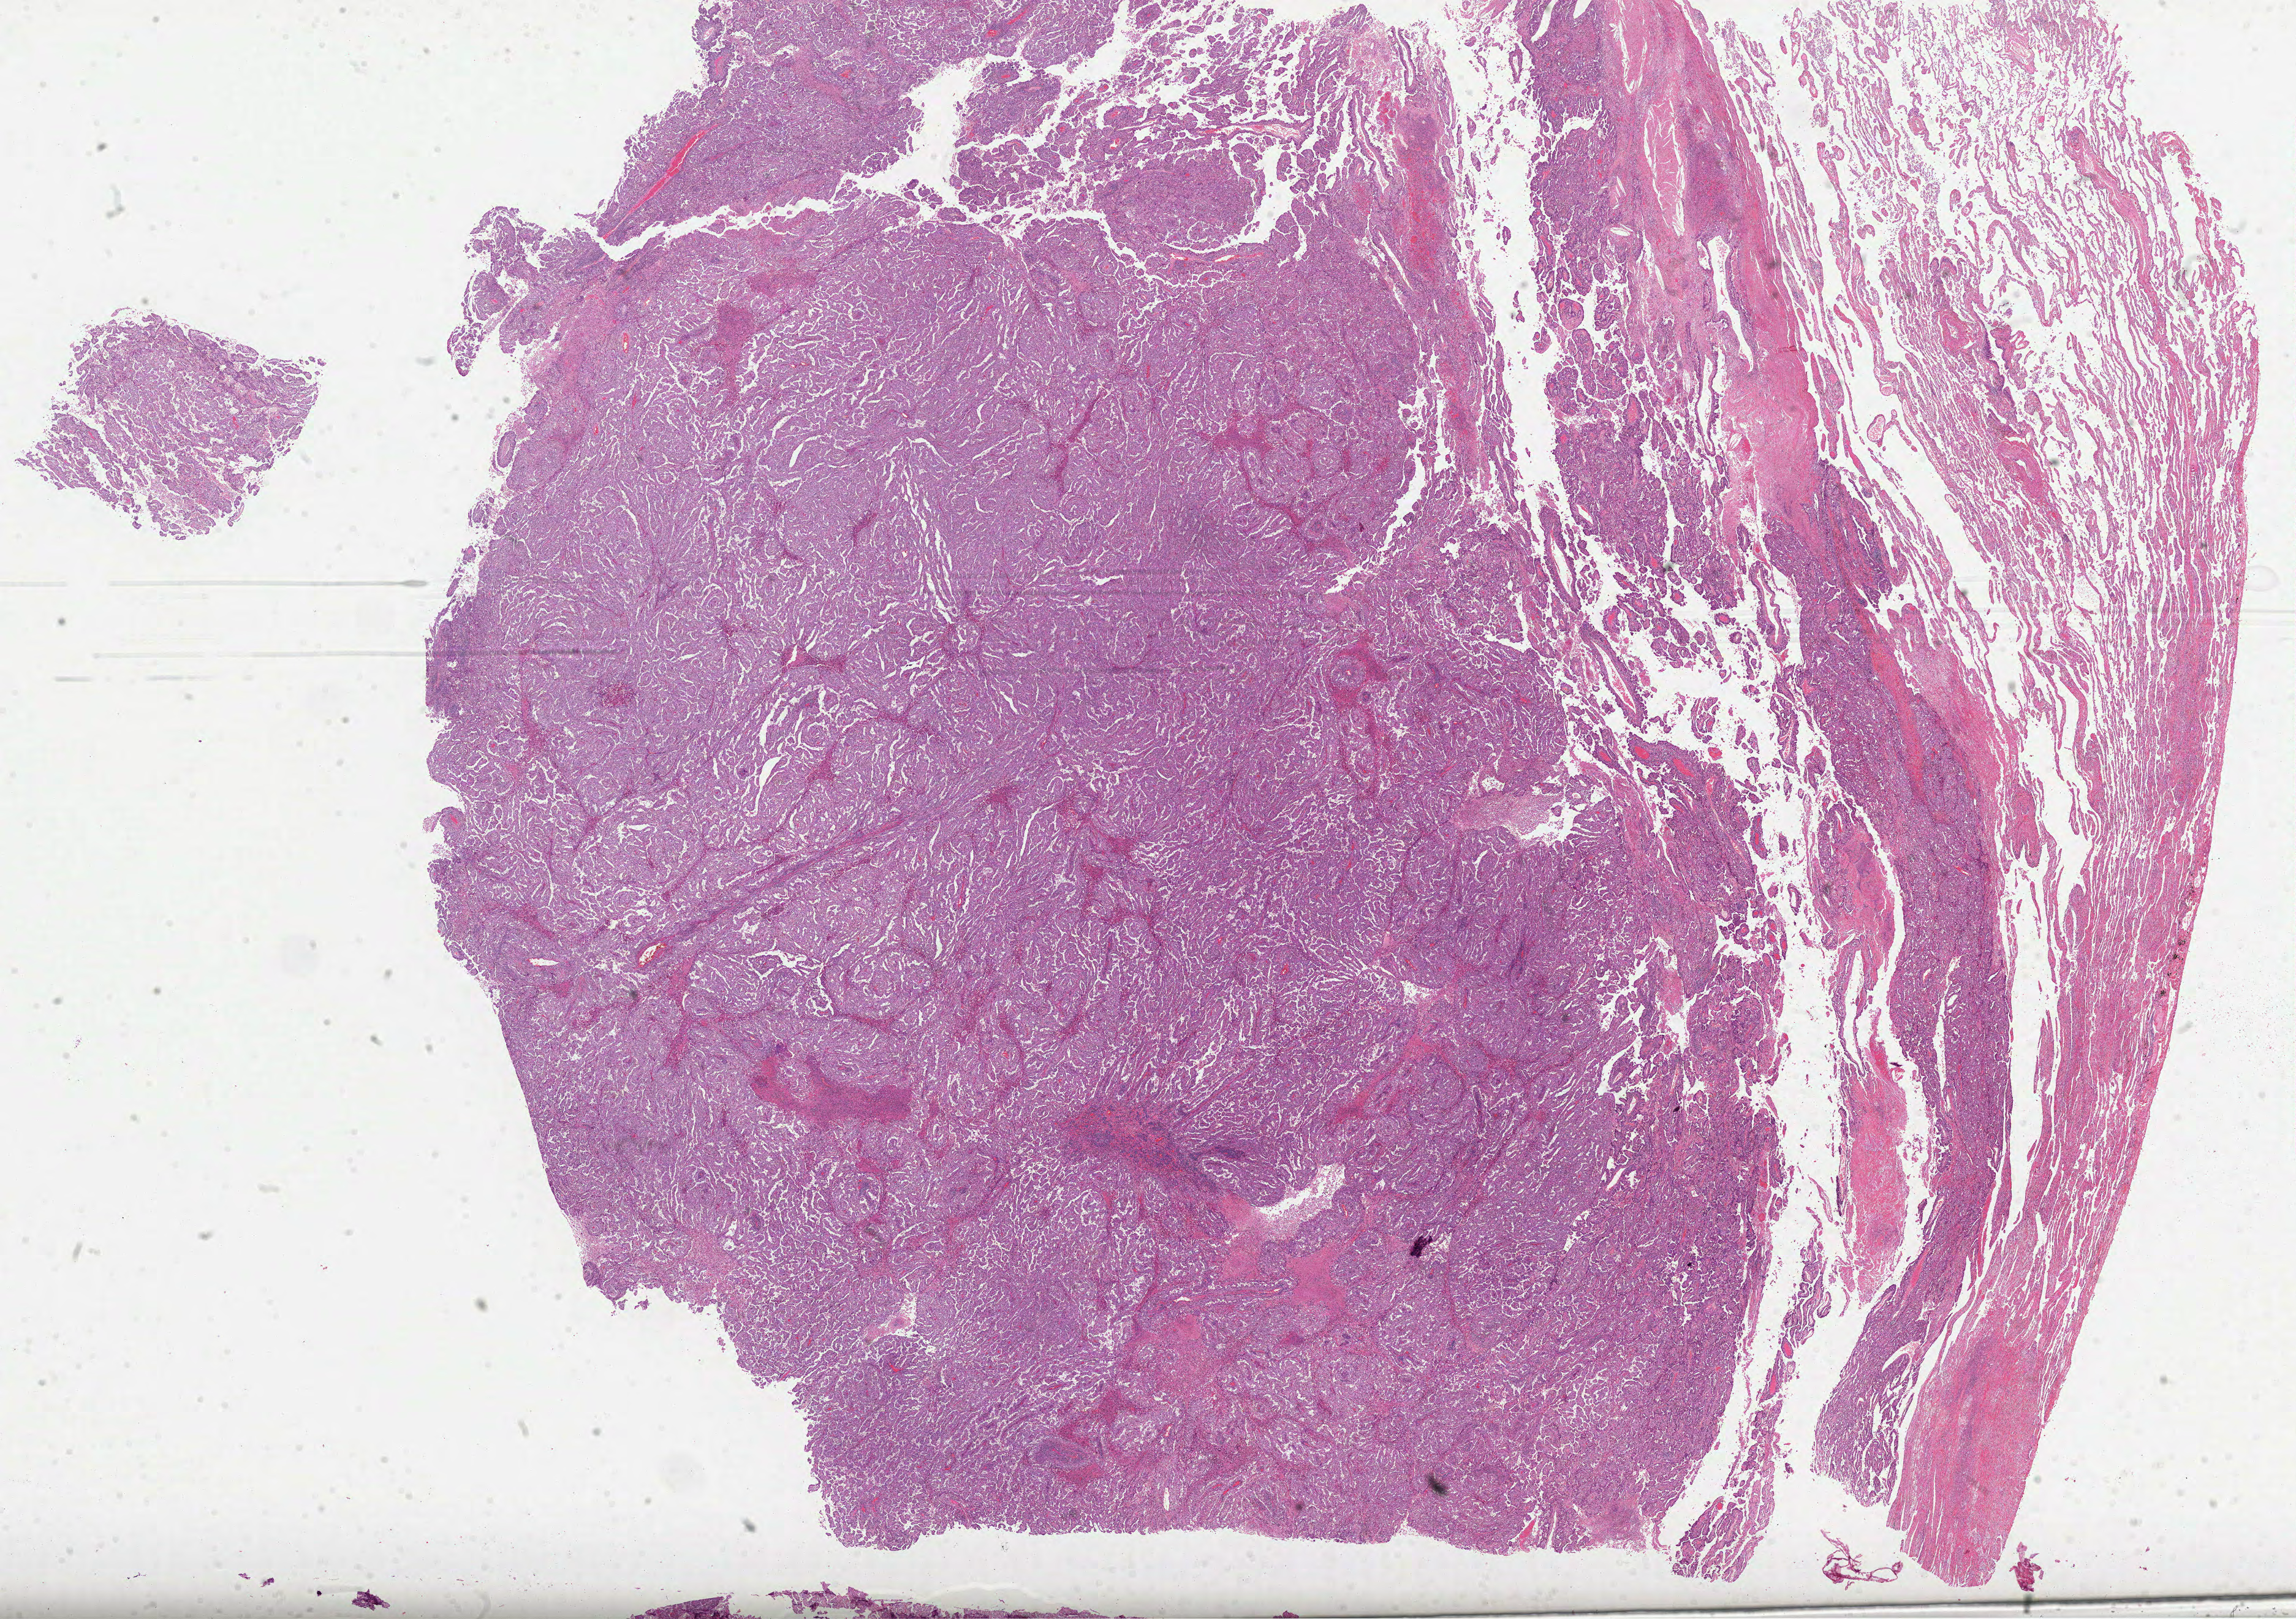
H&E-stained whole-slide image — shown as a low-resolution overview of the whole scanned area (about 30.2 x 21.3 mm, slide scanned at 40x), formalin-fixed paraffin-embedded (FFPE) diagnostic section, sample: primary tumour, lung. Male patient; age at initial diagnosis 72 years.
Laterality: left. AJCC pathologic stage: IIIA (6th edition). Pathologic diagnosis: Adenocarcinoma, NOS (upper lobe, lung).